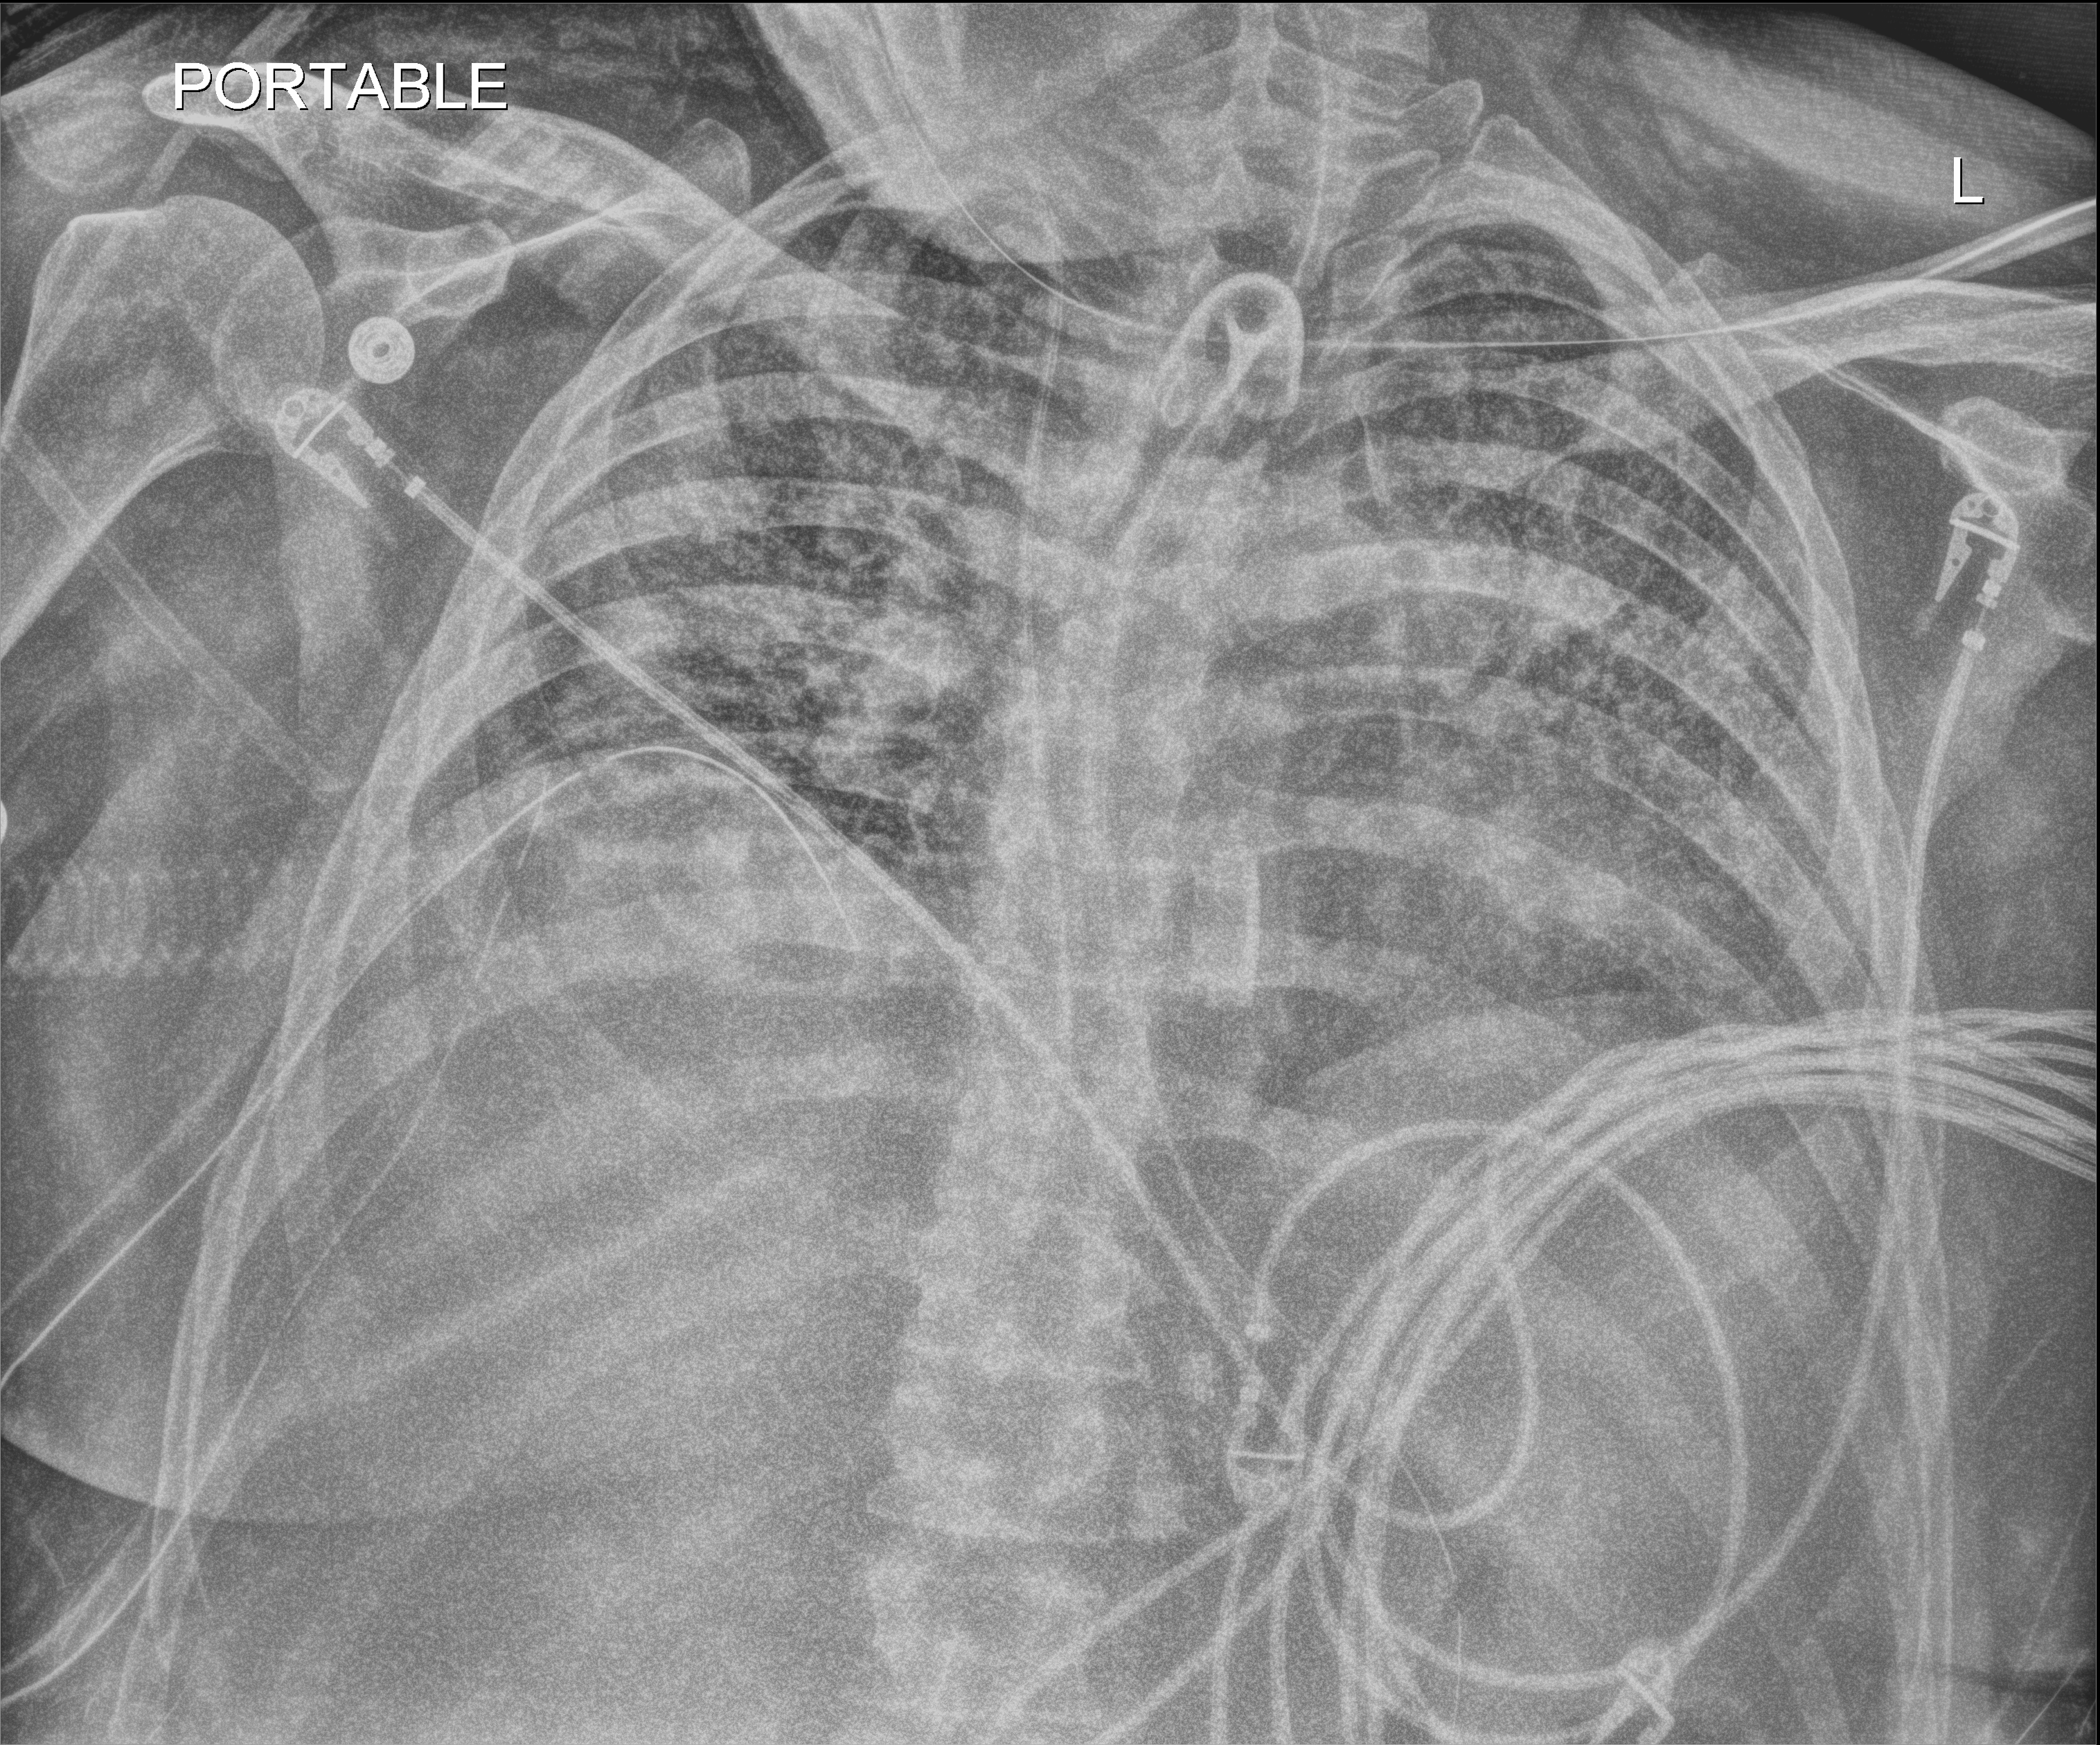
Bedside chest radiograph (digital radiography). Patient hospitalised with COVID-19; male, aged 18–59 years.
Admission-level facts for this patient (not findings on this image; timing relative to this image not recorded): admitted to intensive care during this hospital stay: yes; length of hospital stay: 80 days.